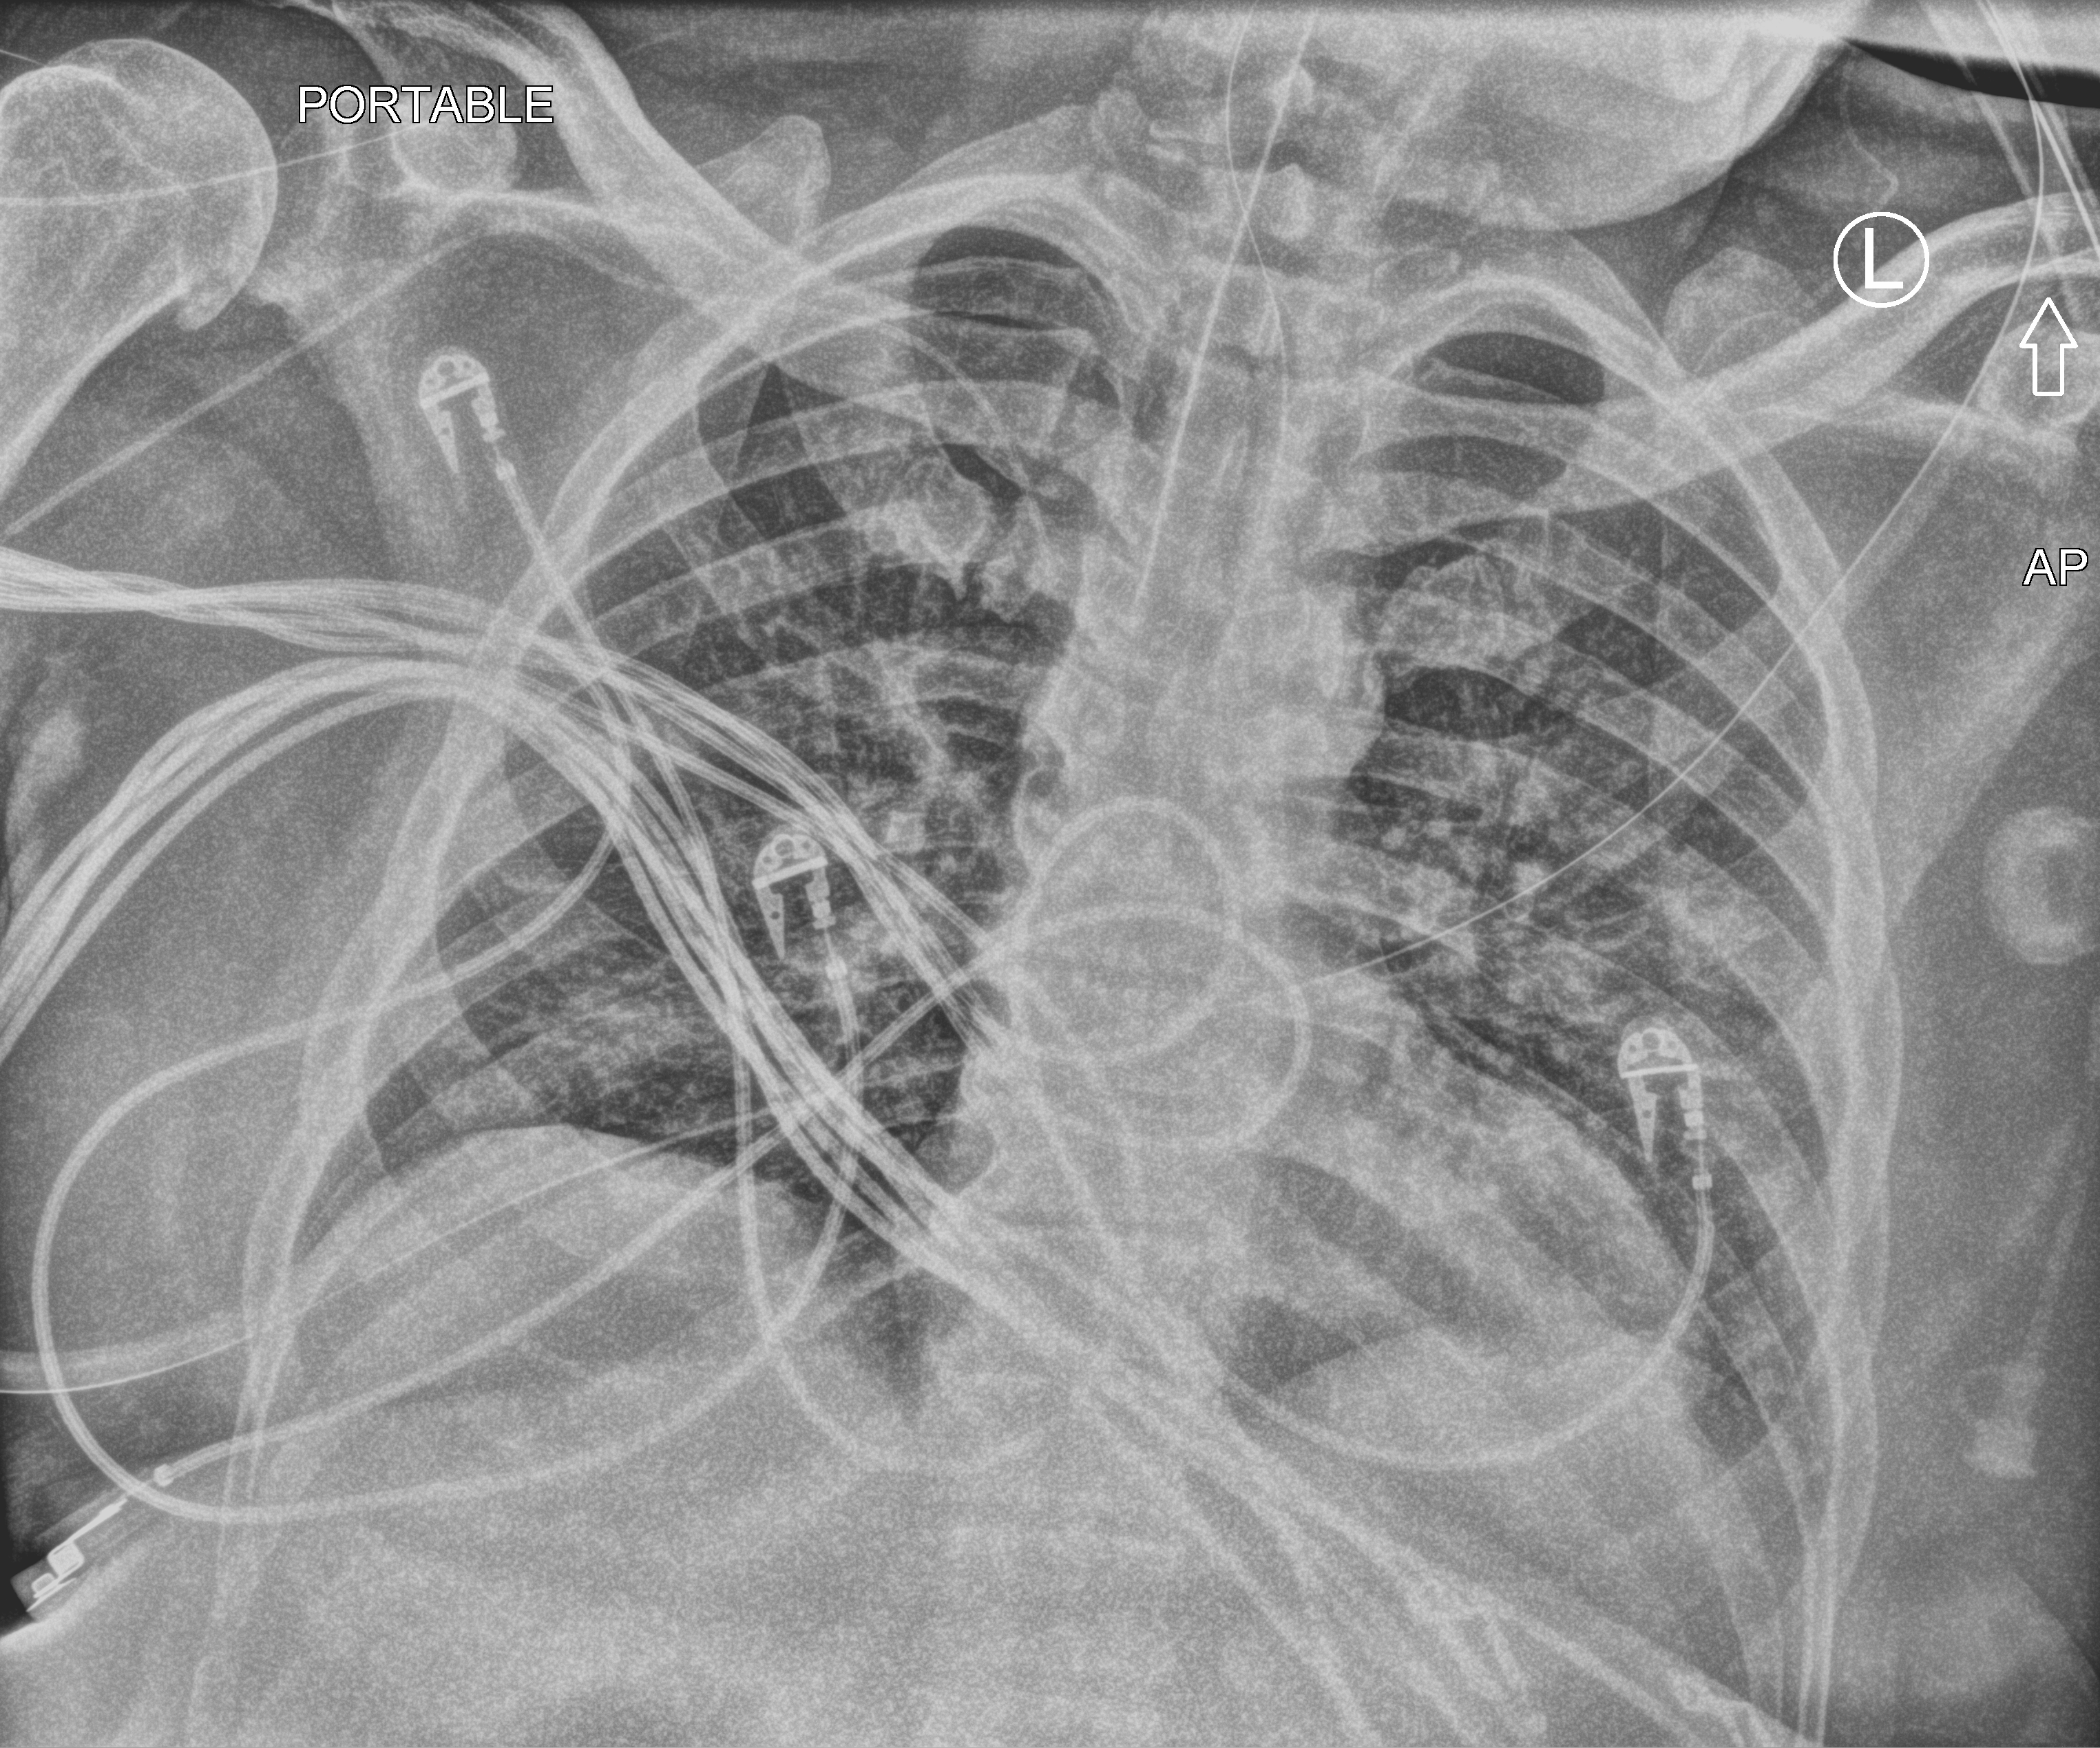
Chest X-ray (portable), anteroposterior (AP) projection. Male patient hospitalised with COVID-19, age 18–59 years.
Admission-level facts for this patient (not findings on this image; timing relative to this image not recorded): diabetes (admission record): no; admitted to intensive care during this hospital stay: yes; smoking status (admission record): never.